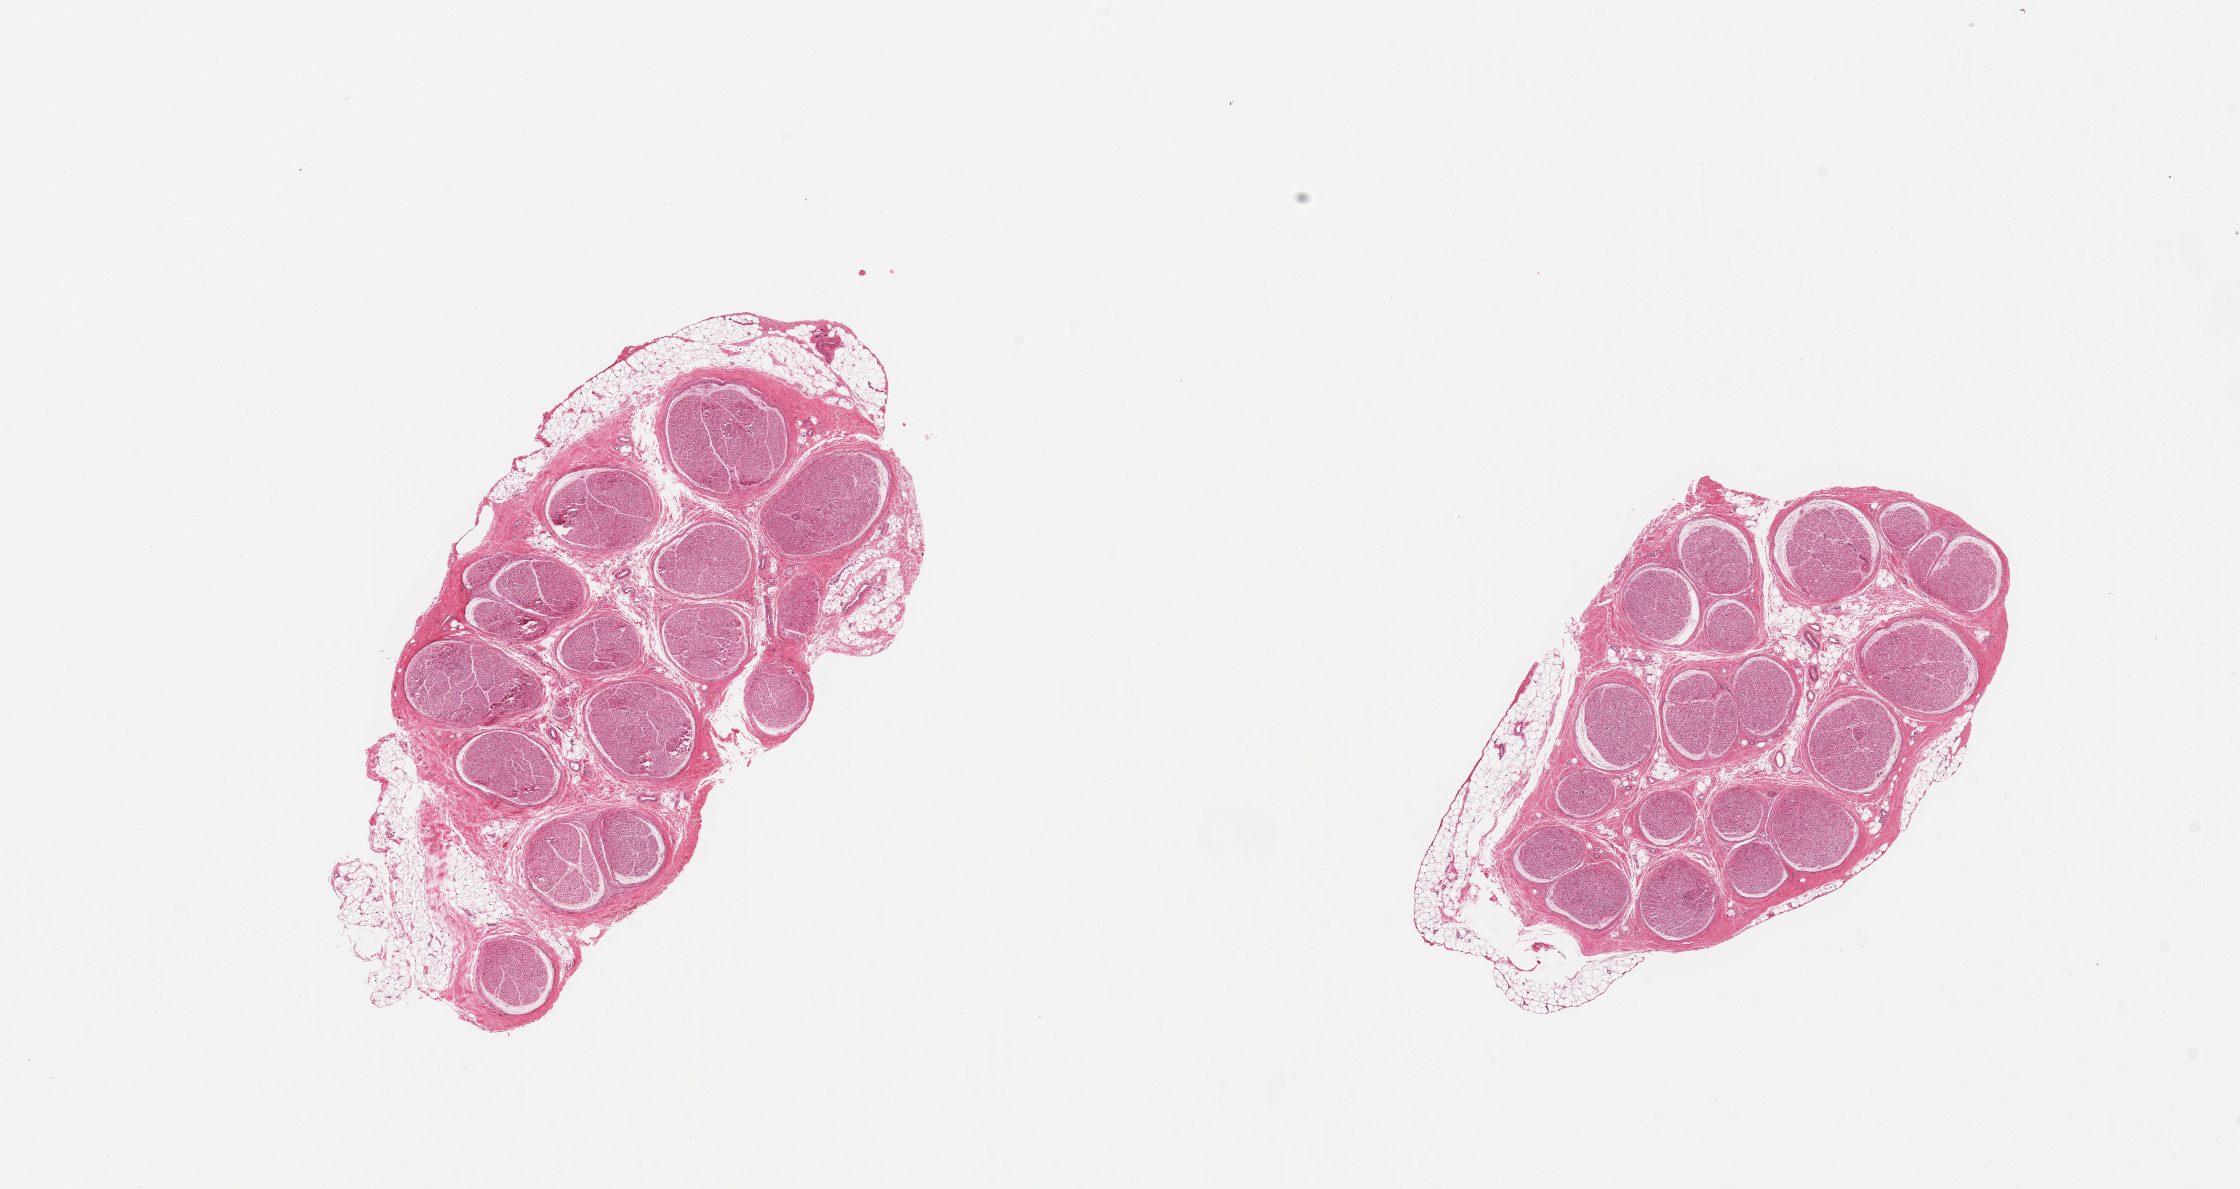
Hematoxylin and eosin (H&E) whole-slide image, a low-resolution overview of the entire scanned area, about 17.7 x 9.4 mm, PAXgene-fixed paraffin-embedded (PFPE) section, sampled site (target tissue): tibial nerve, tissue donor sample. Donor sex: female.
- reviewer comment on this tissue sample: 2 pieces; 10% internal & external fat